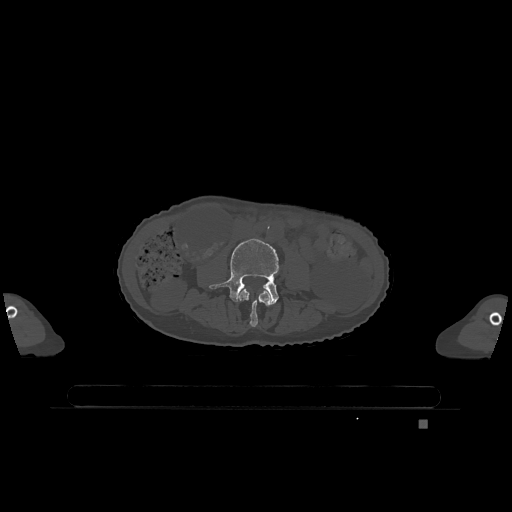
CT including the spine, one axial slice. Slice 319 of 1317 in the series (ordered by position). Bone window (W 1800 / L 400 HU). 0.5 mm slice thickness. 512 × 512 image matrix, field of view 500 × 500 mm. Patient: female, 74 years. Case-level facts recorded for this patient, not image findings: primary cancer: lung.
Annotated regions visible in this slice (semi-automatic segmentation, software-assisted and operator-edited):
- L3 vertebra: bounding box <238,289,271,327> (left, top, right, bottom; pixels)
- L4 vertebra: <209,239,279,305>